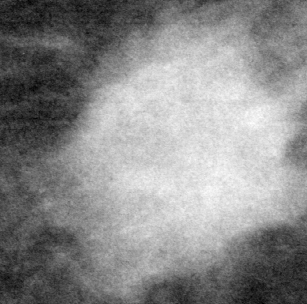
Region of interest cut from a scanned film mammogram (one marked finding), left breast, CC view, BI-RADS breast density category 2 (scale 1–4).
Finding: mass, shape lobulated / architectural distortion, margins microlobulated / spiculated; BI-RADS assessment category 4; pathology (as recorded): malignant.